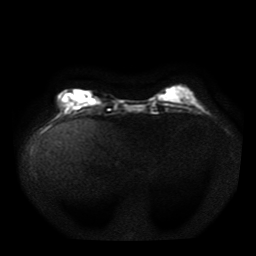
Breast MRI, one axial slice; slice 12 of 41 in the series (ordered by position); diffusion-weighted series; image 2 of 4 stored at this slice position (different b-values; order by instance number); 1.5 T; 5 mm slice thickness; 256 × 256 image matrix, field of view 330 × 330 mm. Female patient.
Structures marked on this image (manually delineated by an expert):
- tumour on diffusion-weighted imaging: bounding box [x1, y1, x2, y2] px = [61, 92, 96, 104]